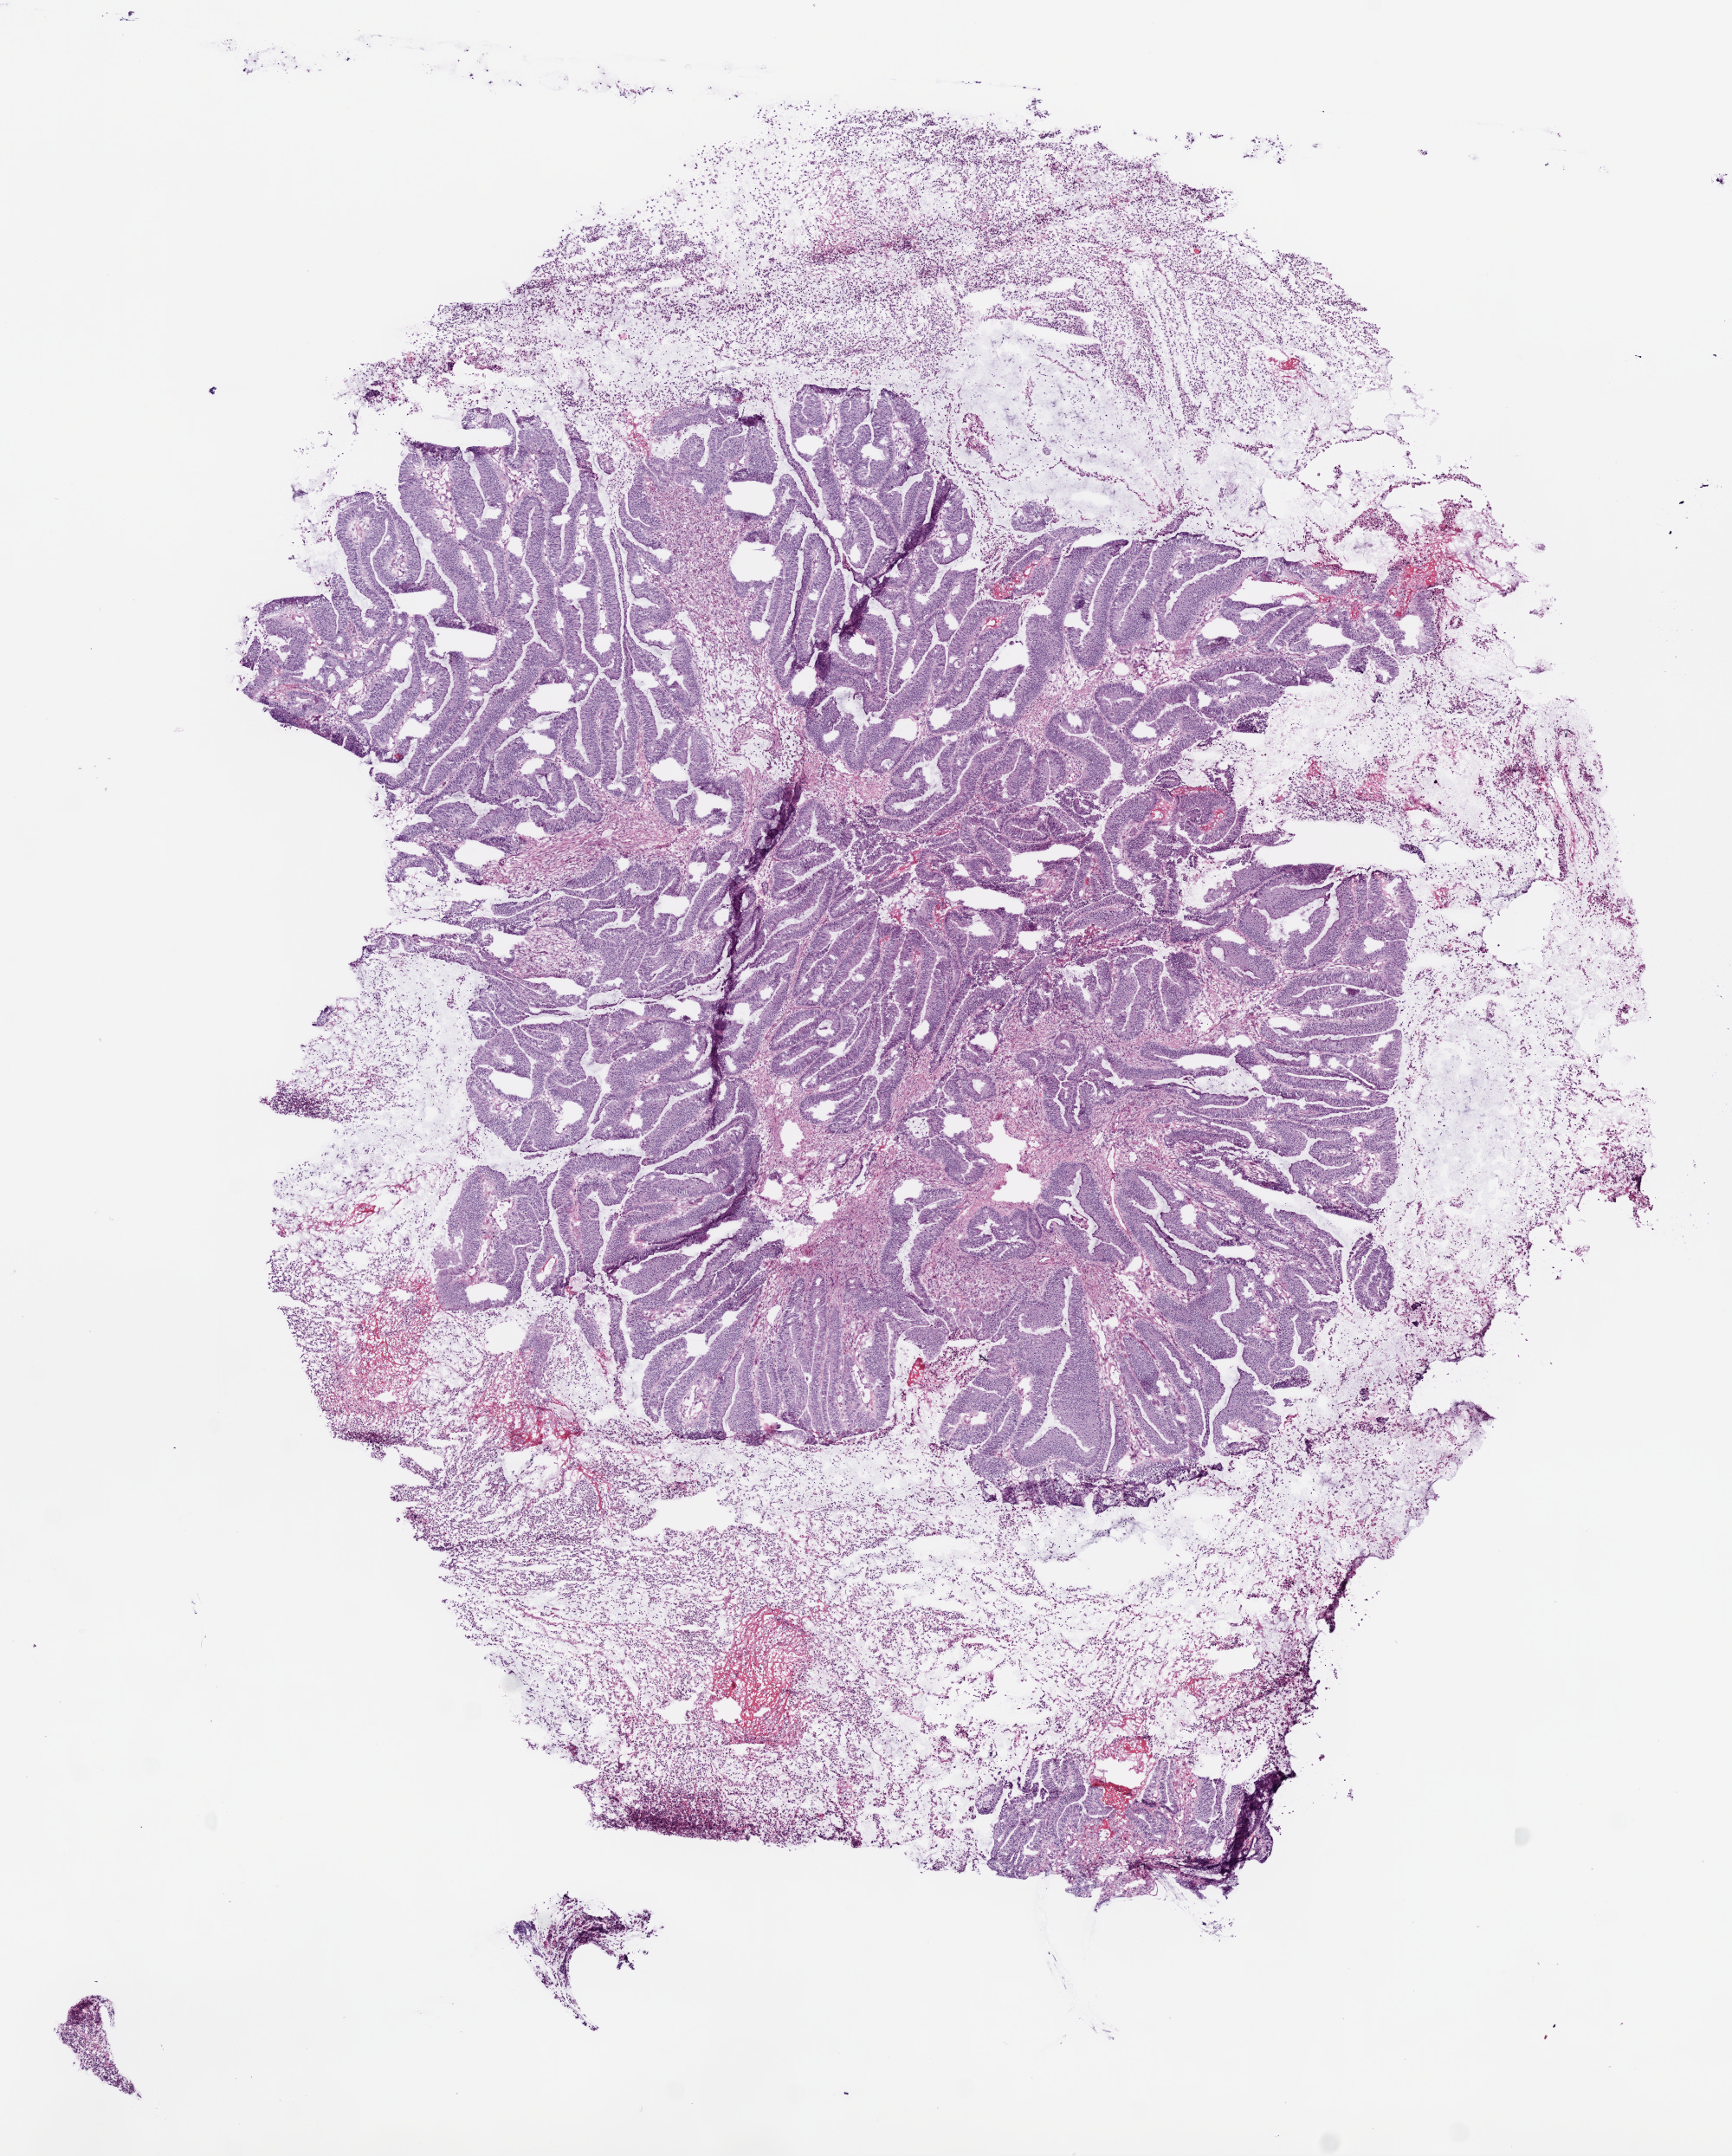
Digitized H&E-stained tissue section (whole slide) — a low-resolution overview of the entire scanned area, about 8.0 x 10.0 mm; frozen section from the top of the tissue portion; primary tumour sample from the colon. Patient: female, age at initial diagnosis 81 years. Slide review estimates, as recorded: tumour cells 60%, tumour nuclei 80%, normal cells 0%, stromal cells 40%, necrosis 0%.
• AJCC pathologic stage: IIA (6th edition)
• diagnosis: Adenocarcinoma, NOS